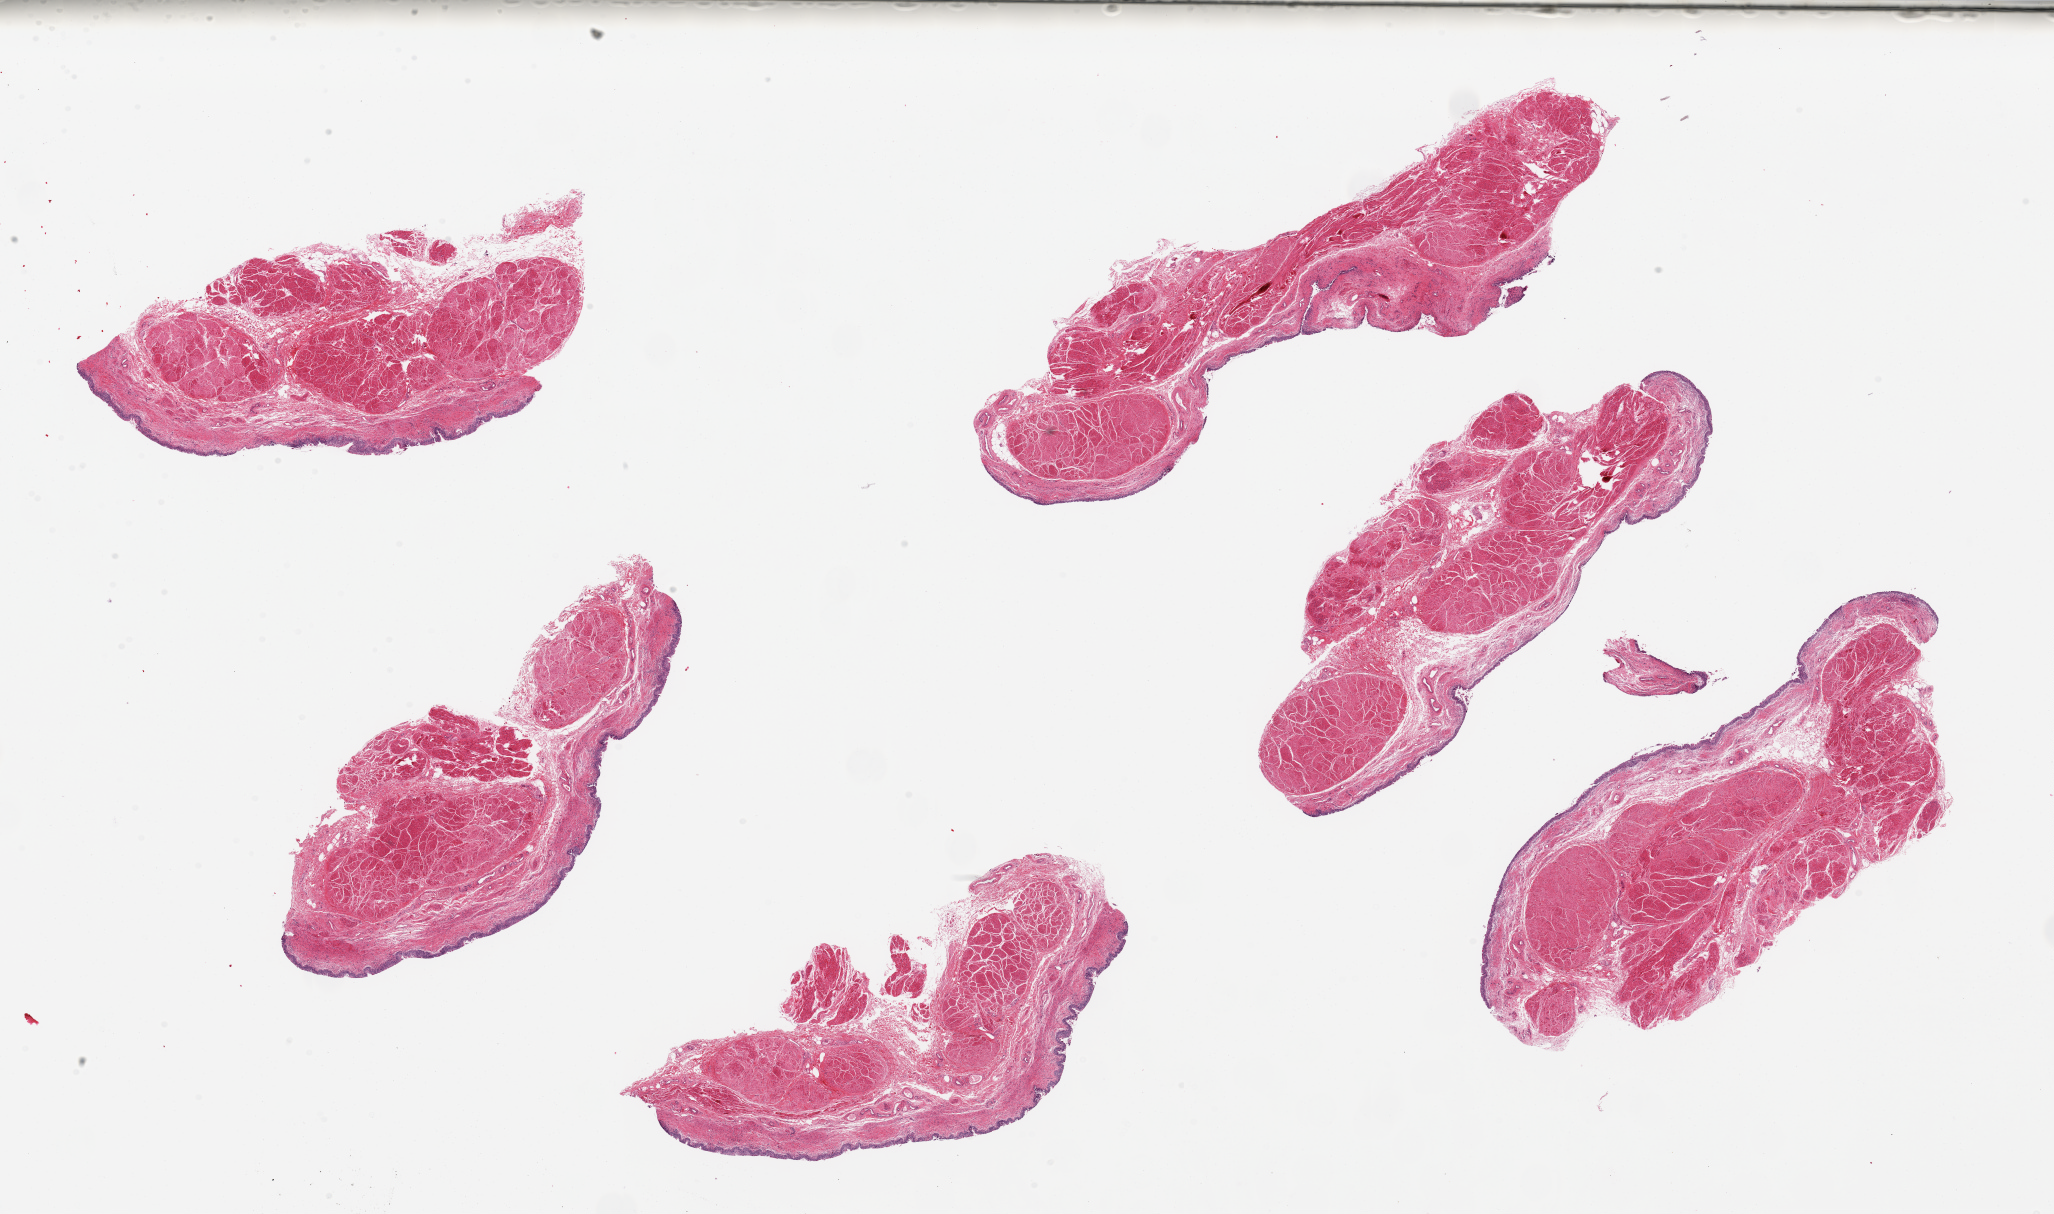
Whole-slide image, H&E stain — low-resolution overview of the scanned area, about 32.5 x 19.2 mm (from a 20x scan); PAXgene-fixed paraffin-embedded (PFPE) section; target tissue: urinary bladder; donor tissue sample.
Review note (as recorded): 6 pieces, ~8x4mm. Urothelium unusually well-preserved, ~2-4% of thickness.